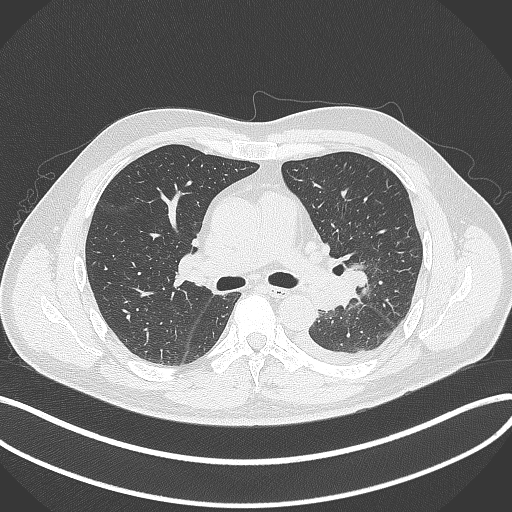
Chest CT, one axial slice. Reconstruction kernel B70f. 120 kVp. Lung window (W 1500 / L -600 HU). 1 mm slice thickness. 512 × 512 image matrix. Male patient, age 58 years. Case-level facts recorded for this patient, not image findings: clinical TNM (as recorded): T3 N1 M1b; histopathological grade: G3.
Structures marked on this image (rectangle marked by the reading radiologist):
- lung tumour (recorded histology: small cell carcinoma): box from (x=340, y=265) to (x=371, y=289) px